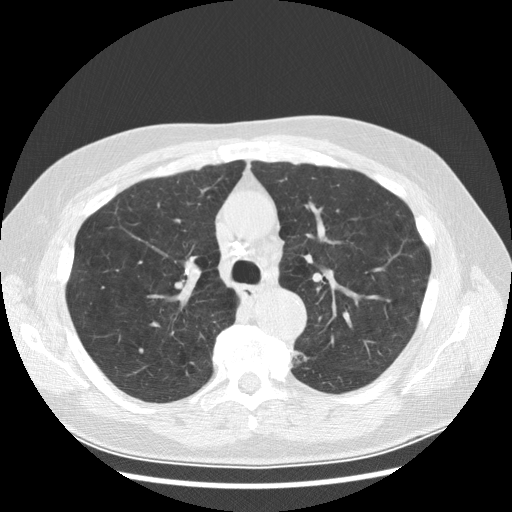
Low-dose screening chest CT, one axial slice. Slice 196 of 282 in the series (ordered by position). 120 kVp. Lung window (W 1500 / L -600 HU). 2.5 mm slice thickness. 512 × 512 image matrix.
Annotated regions visible in this slice (outlined manually by an expert reader):
- lesion 1 (tumor, lower lobe of left lung): bounding box [x1, y1, x2, y2] px = [294, 350, 308, 363]